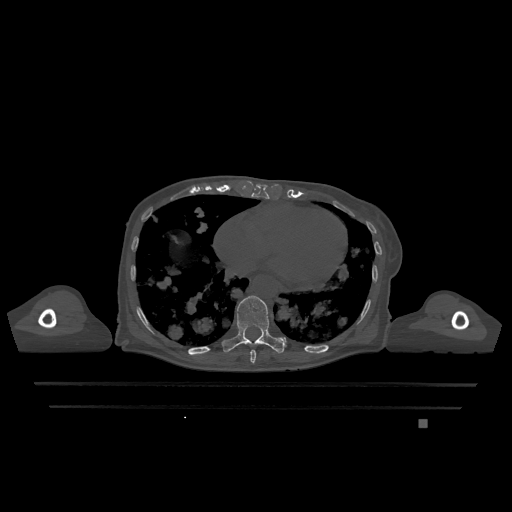
CT including the spine, one axial slice; bone window (W 1800 / L 400 HU); 512 × 512 image matrix, field of view 500 × 500 mm. Female patient, age 74 years. From the clinical record (not read from this slice): primary cancer: lung; vertebrae with lytic lesions (as recorded): T1, T4, T5, T6, L4, L5.
Outlined on this slice (semi-automatically segmented with operator editing):
- T10 vertebra: bounding box <222,296,286,353> (left, top, right, bottom; pixels)
- T9 vertebra: <250,350,256,364>